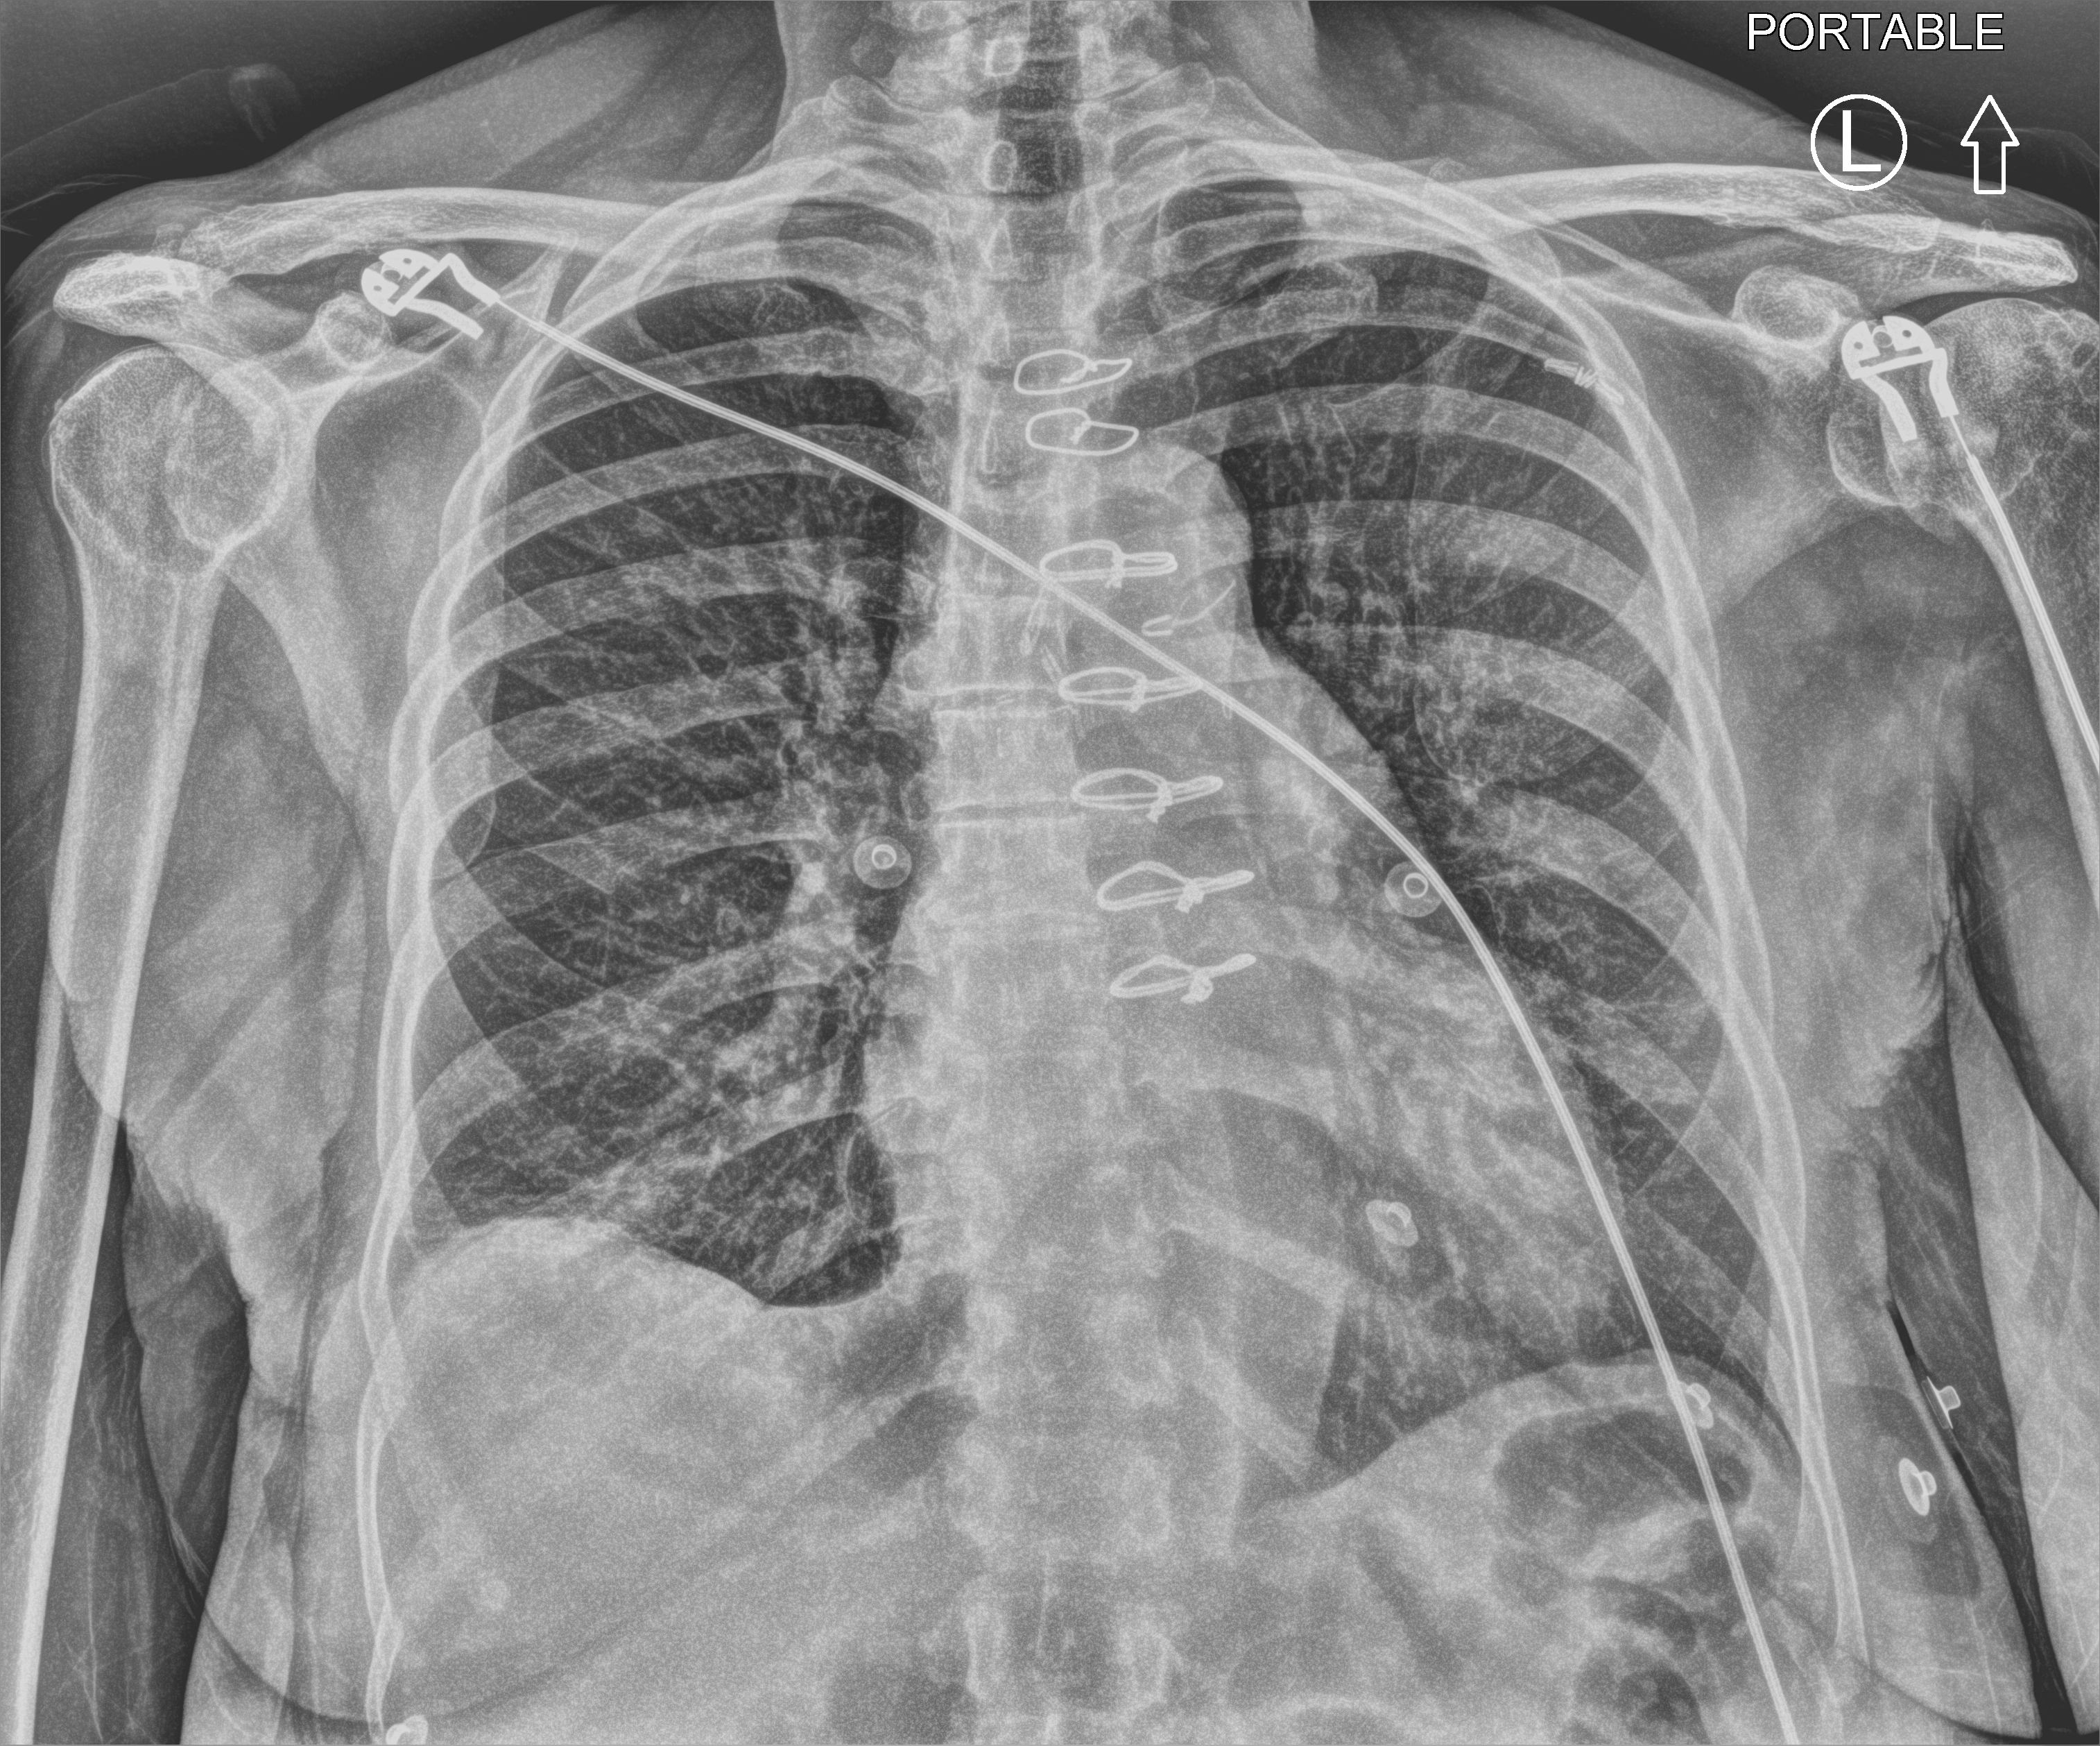
Portable chest radiograph, anteroposterior (AP) projection. Female patient hospitalised with COVID-19, age 60–74 years.
Admission-level facts for this patient (not findings on this image; timing relative to this image not recorded): admitted to intensive care during this hospital stay: no; other chronic lung disease (admission record): no; mechanically ventilated during this hospital stay: no.